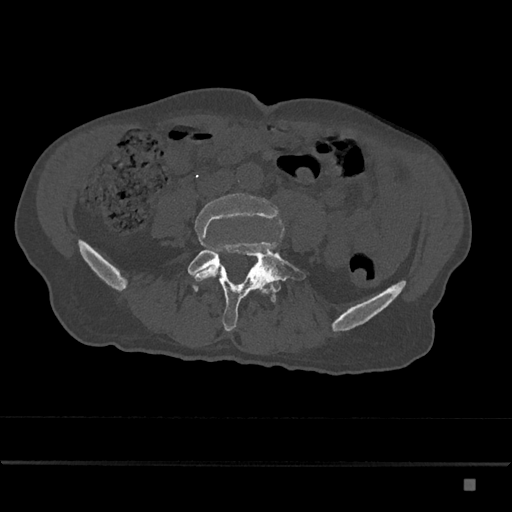
CT including the spine, one axial slice; position 298 of 797 along the scan axis; bone window (W 1800 / L 400 HU); 0.5 mm slice thickness; 512 × 512 image matrix. Male patient, age 72 years. Case-level facts recorded for this patient, not image findings: primary cancer: prostate.
Annotated regions visible in this slice (semi-automatically segmented with operator editing):
- L4 vertebra: bounding box <192,193,280,282> (left, top, right, bottom; pixels)
- L5 vertebra: <187,241,306,331>